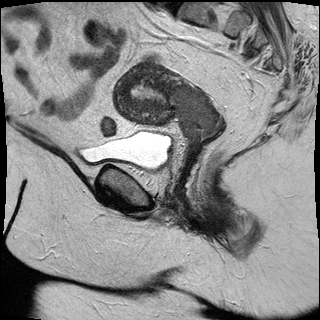
Pelvic MRI for cervical cancer, one sagittal slice; slice 12 of 30 in the series (ordered by position); T2-weighted; 1.5 T; TE 89 ms, TR 2930 ms; 4 mm slice thickness; 320 × 320 image matrix, field of view 260 × 260 mm. Patient: female, 53 years.
Annotated regions visible in this slice (manually delineated by an expert):
- uterus and cervix: bounding box <113,61,221,144> (left, top, right, bottom; pixels)